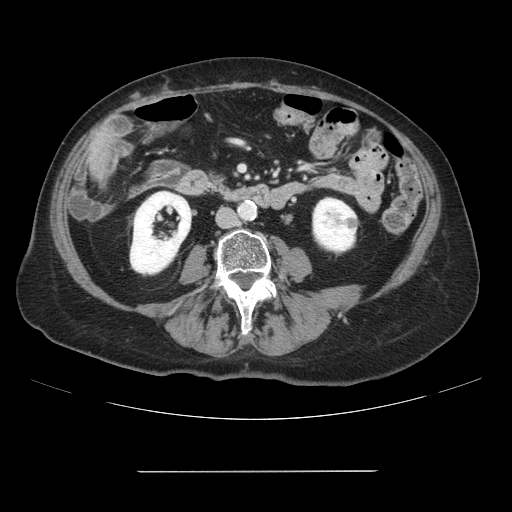
Contrast-enhanced abdominal CT, one axial slice; position 6 of 111 along the scan axis; intravenous contrast given; soft-tissue window (W 400 / L 40 HU); 512 × 512 image matrix. Female patient, age 74 years. Case-level facts recorded for this patient, not image findings: diagnosis: colorectal cancer liver metastases, imaged before liver resection; multiple liver metastases: yes; largest metastasis: 1.1 cm; disease in both lobes: yes.
Outlined on this slice (manually delineated by an expert):
- liver: bounding box <90,128,113,179> (left, top, right, bottom; pixels)